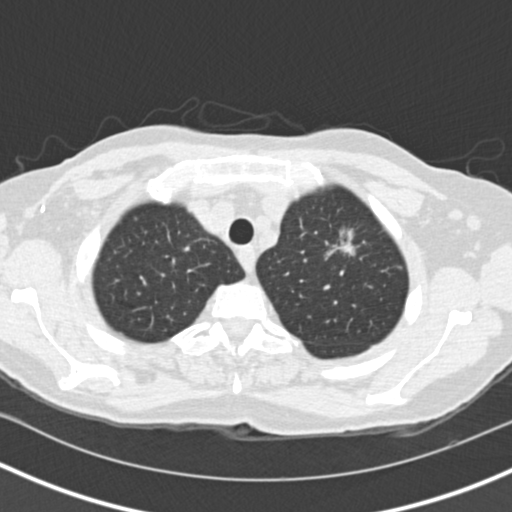
Axial slice from a low-dose chest CT screening exam, baseline screening round, lung window (W 1500 / L -600 HU), 2 mm slice thickness, 512 × 512 image matrix. Female, age 73 years at enrolment. Current smoker at enrolment.
Lesion marked by an expert reader, bounding box <310,224,362,285> (left, top, right, bottom; pixels). The exam's reader record, not a measurement of the box and not confirmed to be the same lesion: non-calcified nodule or mass ≥4 mm, left upper lobe, 27 × 21 mm, spiculated (stellate) margins, soft tissue attenuation. Lung cancer was diagnosed 72 days after this screen: bronchiolo-alveolar adenocarcinoma, NOS, left upper lobe, moderately differentiated (G2), stage IIIB (AJCC 6th edition), 17 mm at pathology.